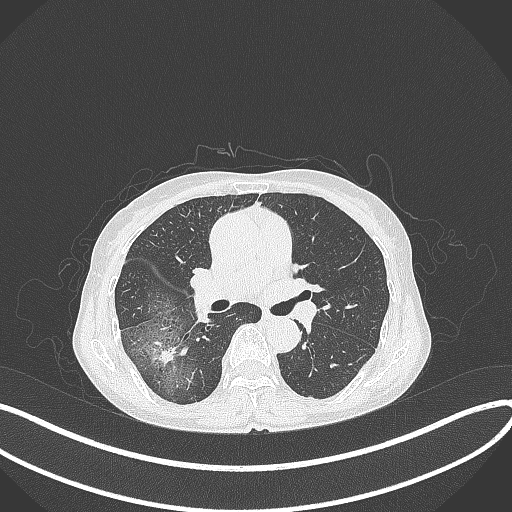
Chest CT, one axial slice. Reconstruction kernel B70f. 120 kVp. Lung window (W 1500 / L -600 HU). 1 mm slice thickness. 512 × 512 image matrix, field of view 400 × 400 mm. Female patient, age 69 years. Case-level facts recorded for this patient, not image findings: clinical TNM (as recorded): T1b N0 M0; histopathological grade: G2-3.
Outlined on this slice (bounding box drawn by a radiologist):
- lung tumour (recorded histology: adenocarcinoma): bounding box <140,332,183,371> (left, top, right, bottom; pixels)